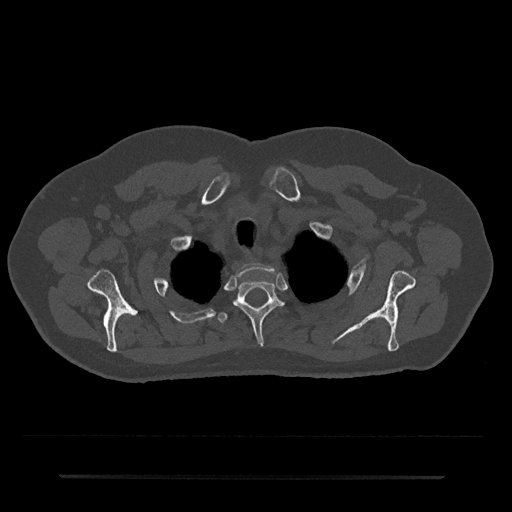
CT including the spine, one axial slice. Slice 604 of 797 in the series (ordered by position). Bone window (W 1800 / L 400 HU). 512 × 512 image matrix, field of view 437 × 437 mm. Patient: male, 69 years. From the clinical record (not read from this slice): primary cancer: prostate.
Outlined on this slice (semi-automatic segmentation, software-assisted and operator-edited):
- T1 vertebra: bounding box <237,263,278,276> (left, top, right, bottom; pixels)
- T2 vertebra: <234,280,284,346>
- T3 vertebra: <218,312,227,323>